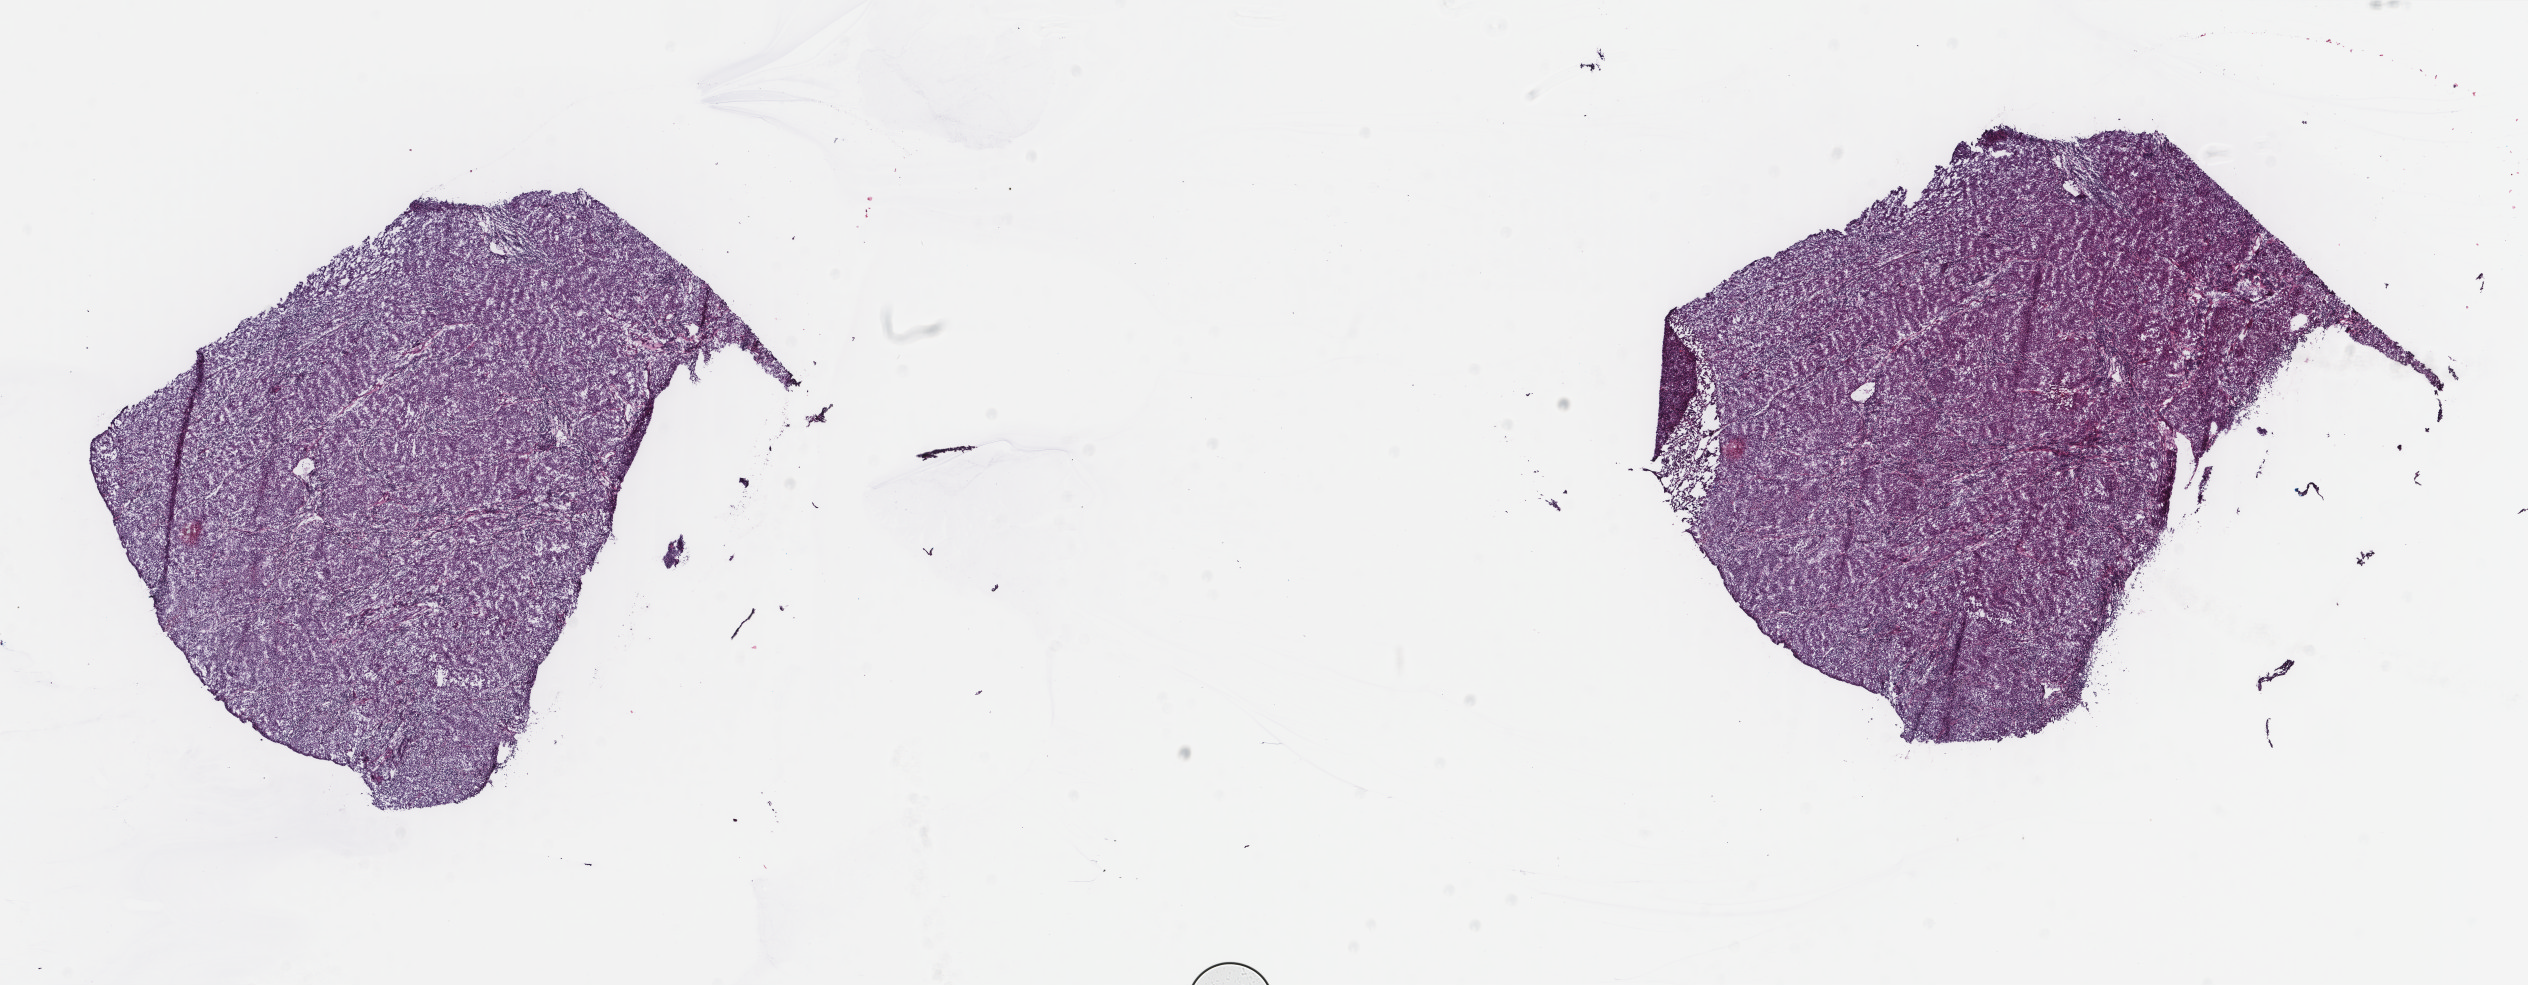
Hematoxylin and eosin (H&E) stained whole-slide image — low-resolution overview of the scanned area, about 20.1 x 7.8 mm (from a 40x scan); frozen section from the top of the tissue portion; metastatic tumour sample, sampled site not recorded. Patient: male, age at initial diagnosis 82 years. Composition of this section per pathologist review: tumour cells 100%, tumour nuclei 90%, normal cells 0%, stromal cells 0%, necrosis 0%. Inflammatory infiltration, as recorded: lymphocyte infiltration 0%, monocyte infiltration 0%, neutrophil infiltration 0%.
* this section: metastatic tumour tissue
* patient diagnosis: Malignant melanoma, NOS